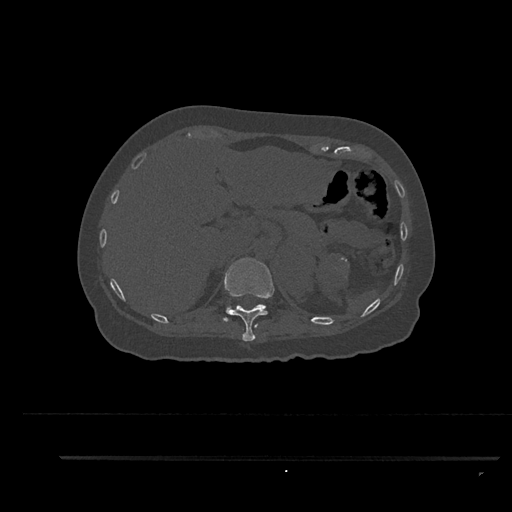
CT including the spine, one axial slice. Slice 305 of 797 in the series (ordered by position). Reconstruction kernel Br40s/3. 120 kVp. Bone window (W 1800 / L 400 HU). 0.5 mm slice thickness. 512 × 512 image matrix, field of view 408 × 408 mm. Patient: female, 44 years. Case-level facts recorded for this patient, not image findings: primary cancer: renal.
Annotated regions visible in this slice (semi-automatically segmented with operator editing):
- T11 vertebra: box from (x=224, y=257) to (x=275, y=341) px
- T12 vertebra: (x=223, y=304)–(x=266, y=322)